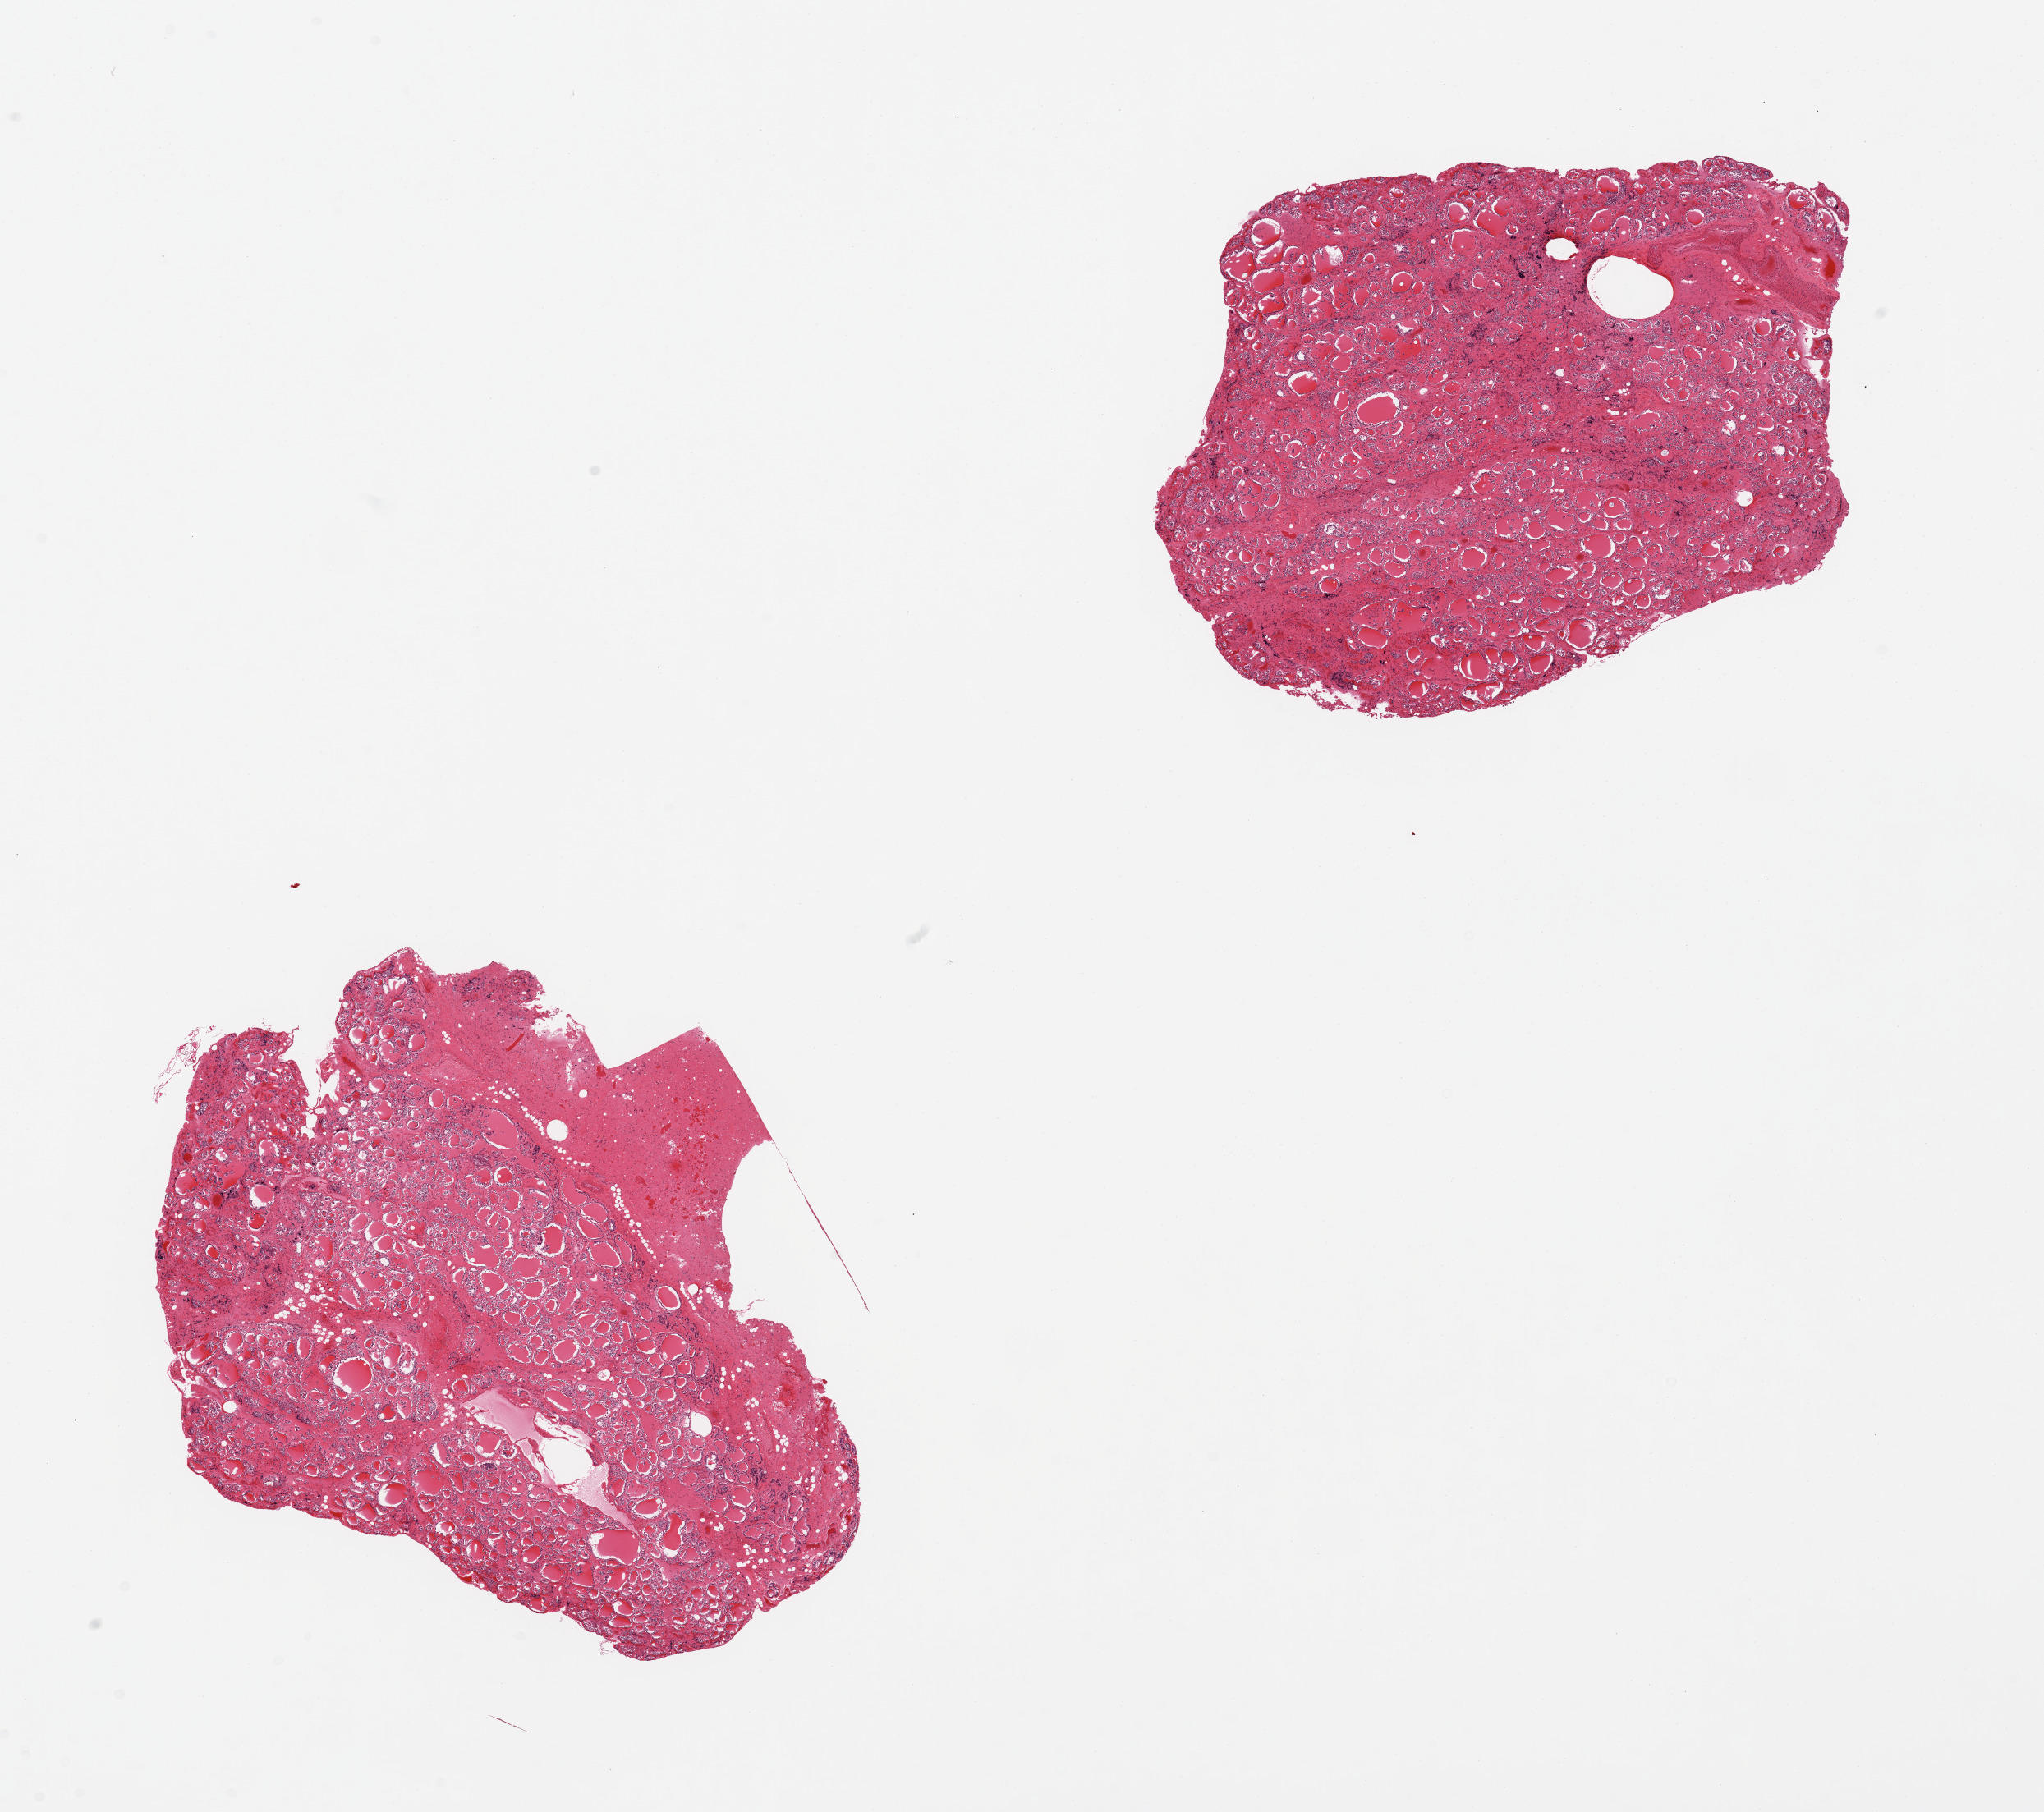
Whole-slide image, H&E stain, brightfield — shown as a low-resolution overview of the whole scanned area (about 19.7 x 17.5 mm, slide scanned at 20x), PAXgene-fixed paraffin-embedded (PFPE) section, sampled site (target tissue): thyroid, tissue donor sample. Donor sex: male.
Reviewer comment on this tissue sample: 2 pieces, moderate autolysis.